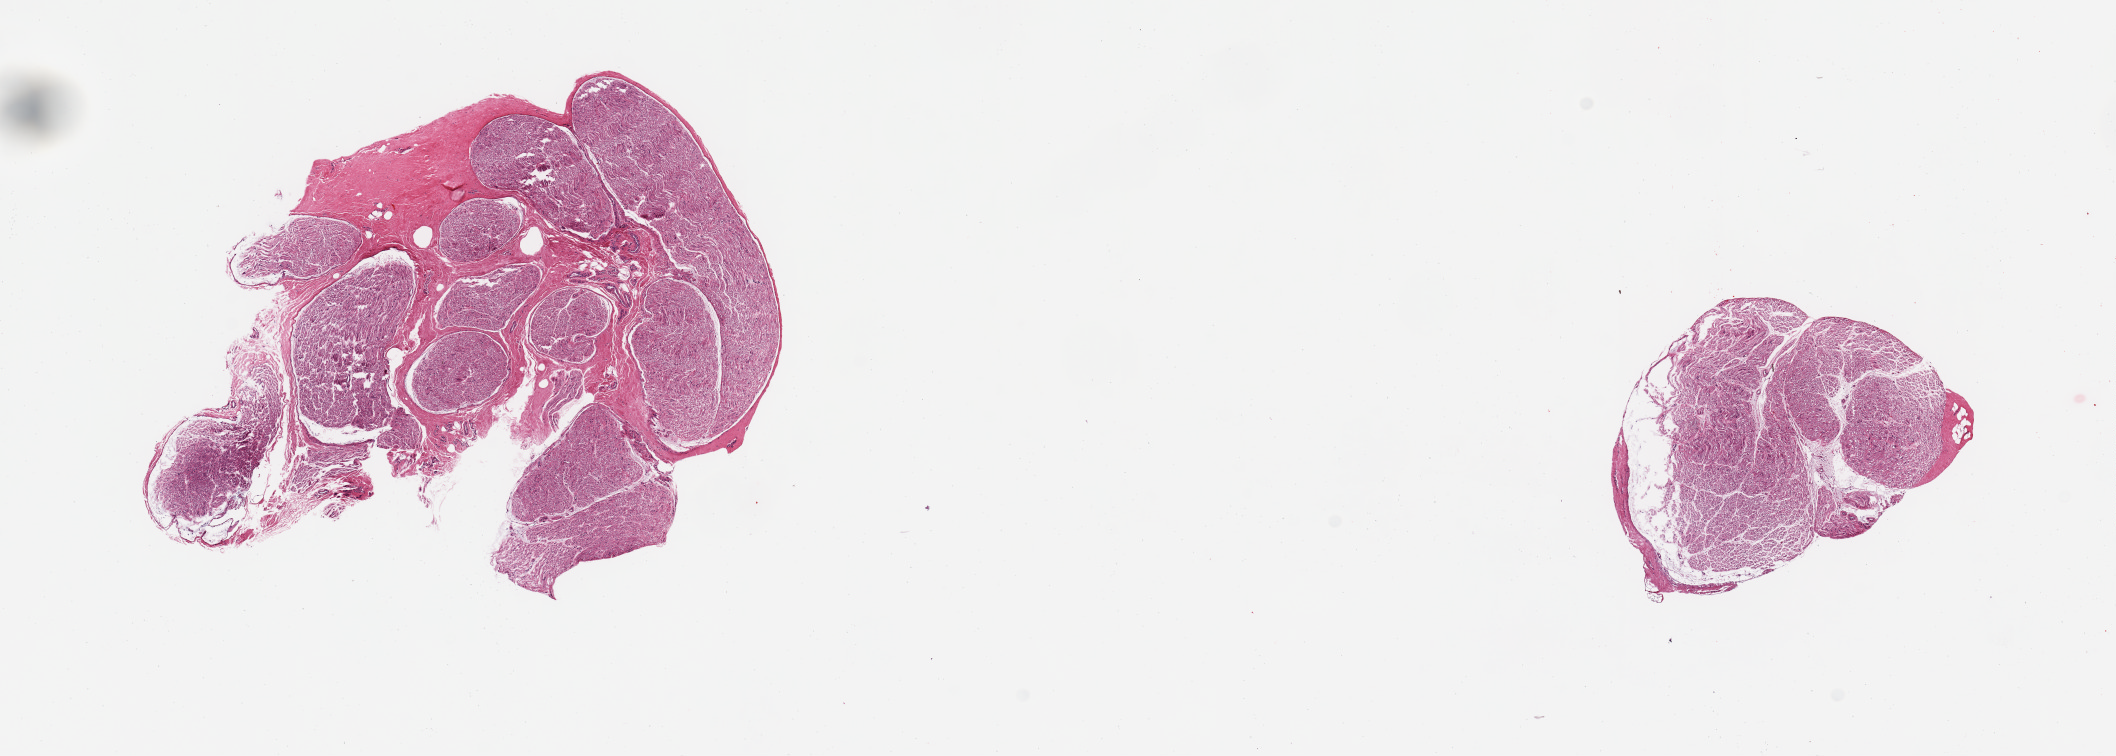
Haematoxylin and eosin whole-slide image, brightfield — whole scanned area (about 16.7 x 6.0 mm, from a 20x scan) shown as a low-resolution overview, PAXgene-fixed, paraffin-embedded tissue, sampled site (target tissue): tibial nerve, tissue donor sample. Male donor.
Review note (as recorded): 2 pieces; 10% ezternal fibrous and fatty content.